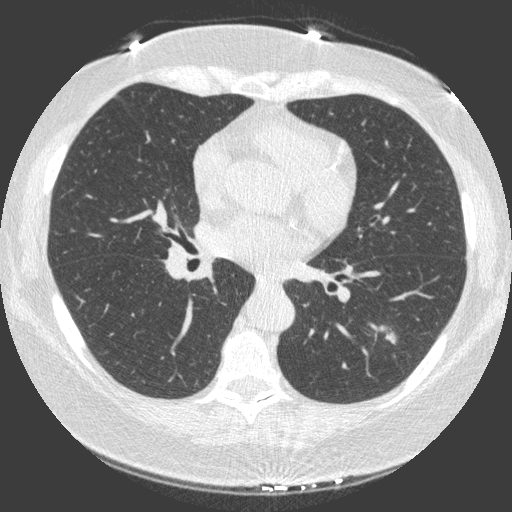
Axial slice from a low-dose chest CT screening exam, third annual screen, lung window (W 1500 / L -600 HU), 1 mm slice thickness. Female participant, aged 66 years at enrolment. Current smoker at enrolment.
Lesion marked by an expert reader, bounding box <360,302,420,358> (left, top, right, bottom; pixels). Screening reader's record for this exam (one nodule recorded; not confirmed to be the boxed lesion): non-calcified nodule or mass ≥4 mm, left lower lobe, 23 × 17 mm, spiculated (stellate) margins, soft tissue attenuation, pre-existing on the prior screen: yes; interval growth: yes. Later outcome: lung cancer diagnosed 15 days after this screen — non-small cell carcinoma, left lower lobe, poorly differentiated (G3), stage IA (AJCC 6th edition), 20 mm at pathology.